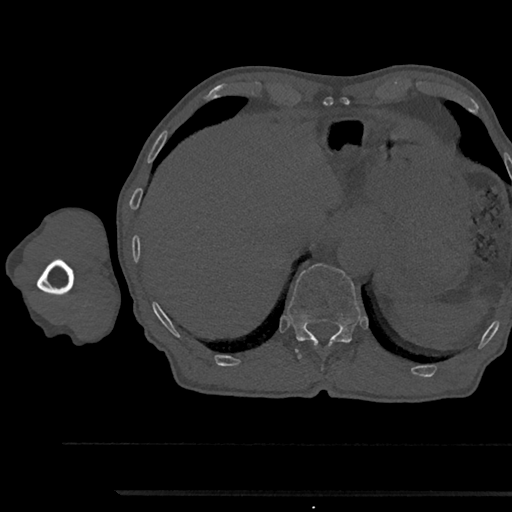
CT including the spine, one axial slice; slice 740 of 797 in the series (ordered by position); reconstruction kernel Br40s/3; bone window (W 1800 / L 400 HU); 0.5 mm slice thickness; 512 × 512 image matrix. Male patient, age 79 years. Case-level facts recorded for this patient, not image findings: primary cancer: prostate.
Outlined on this slice (semi-automatic segmentation, software-assisted and operator-edited):
- T12 vertebra: box from (x=287, y=263) to (x=360, y=359) px